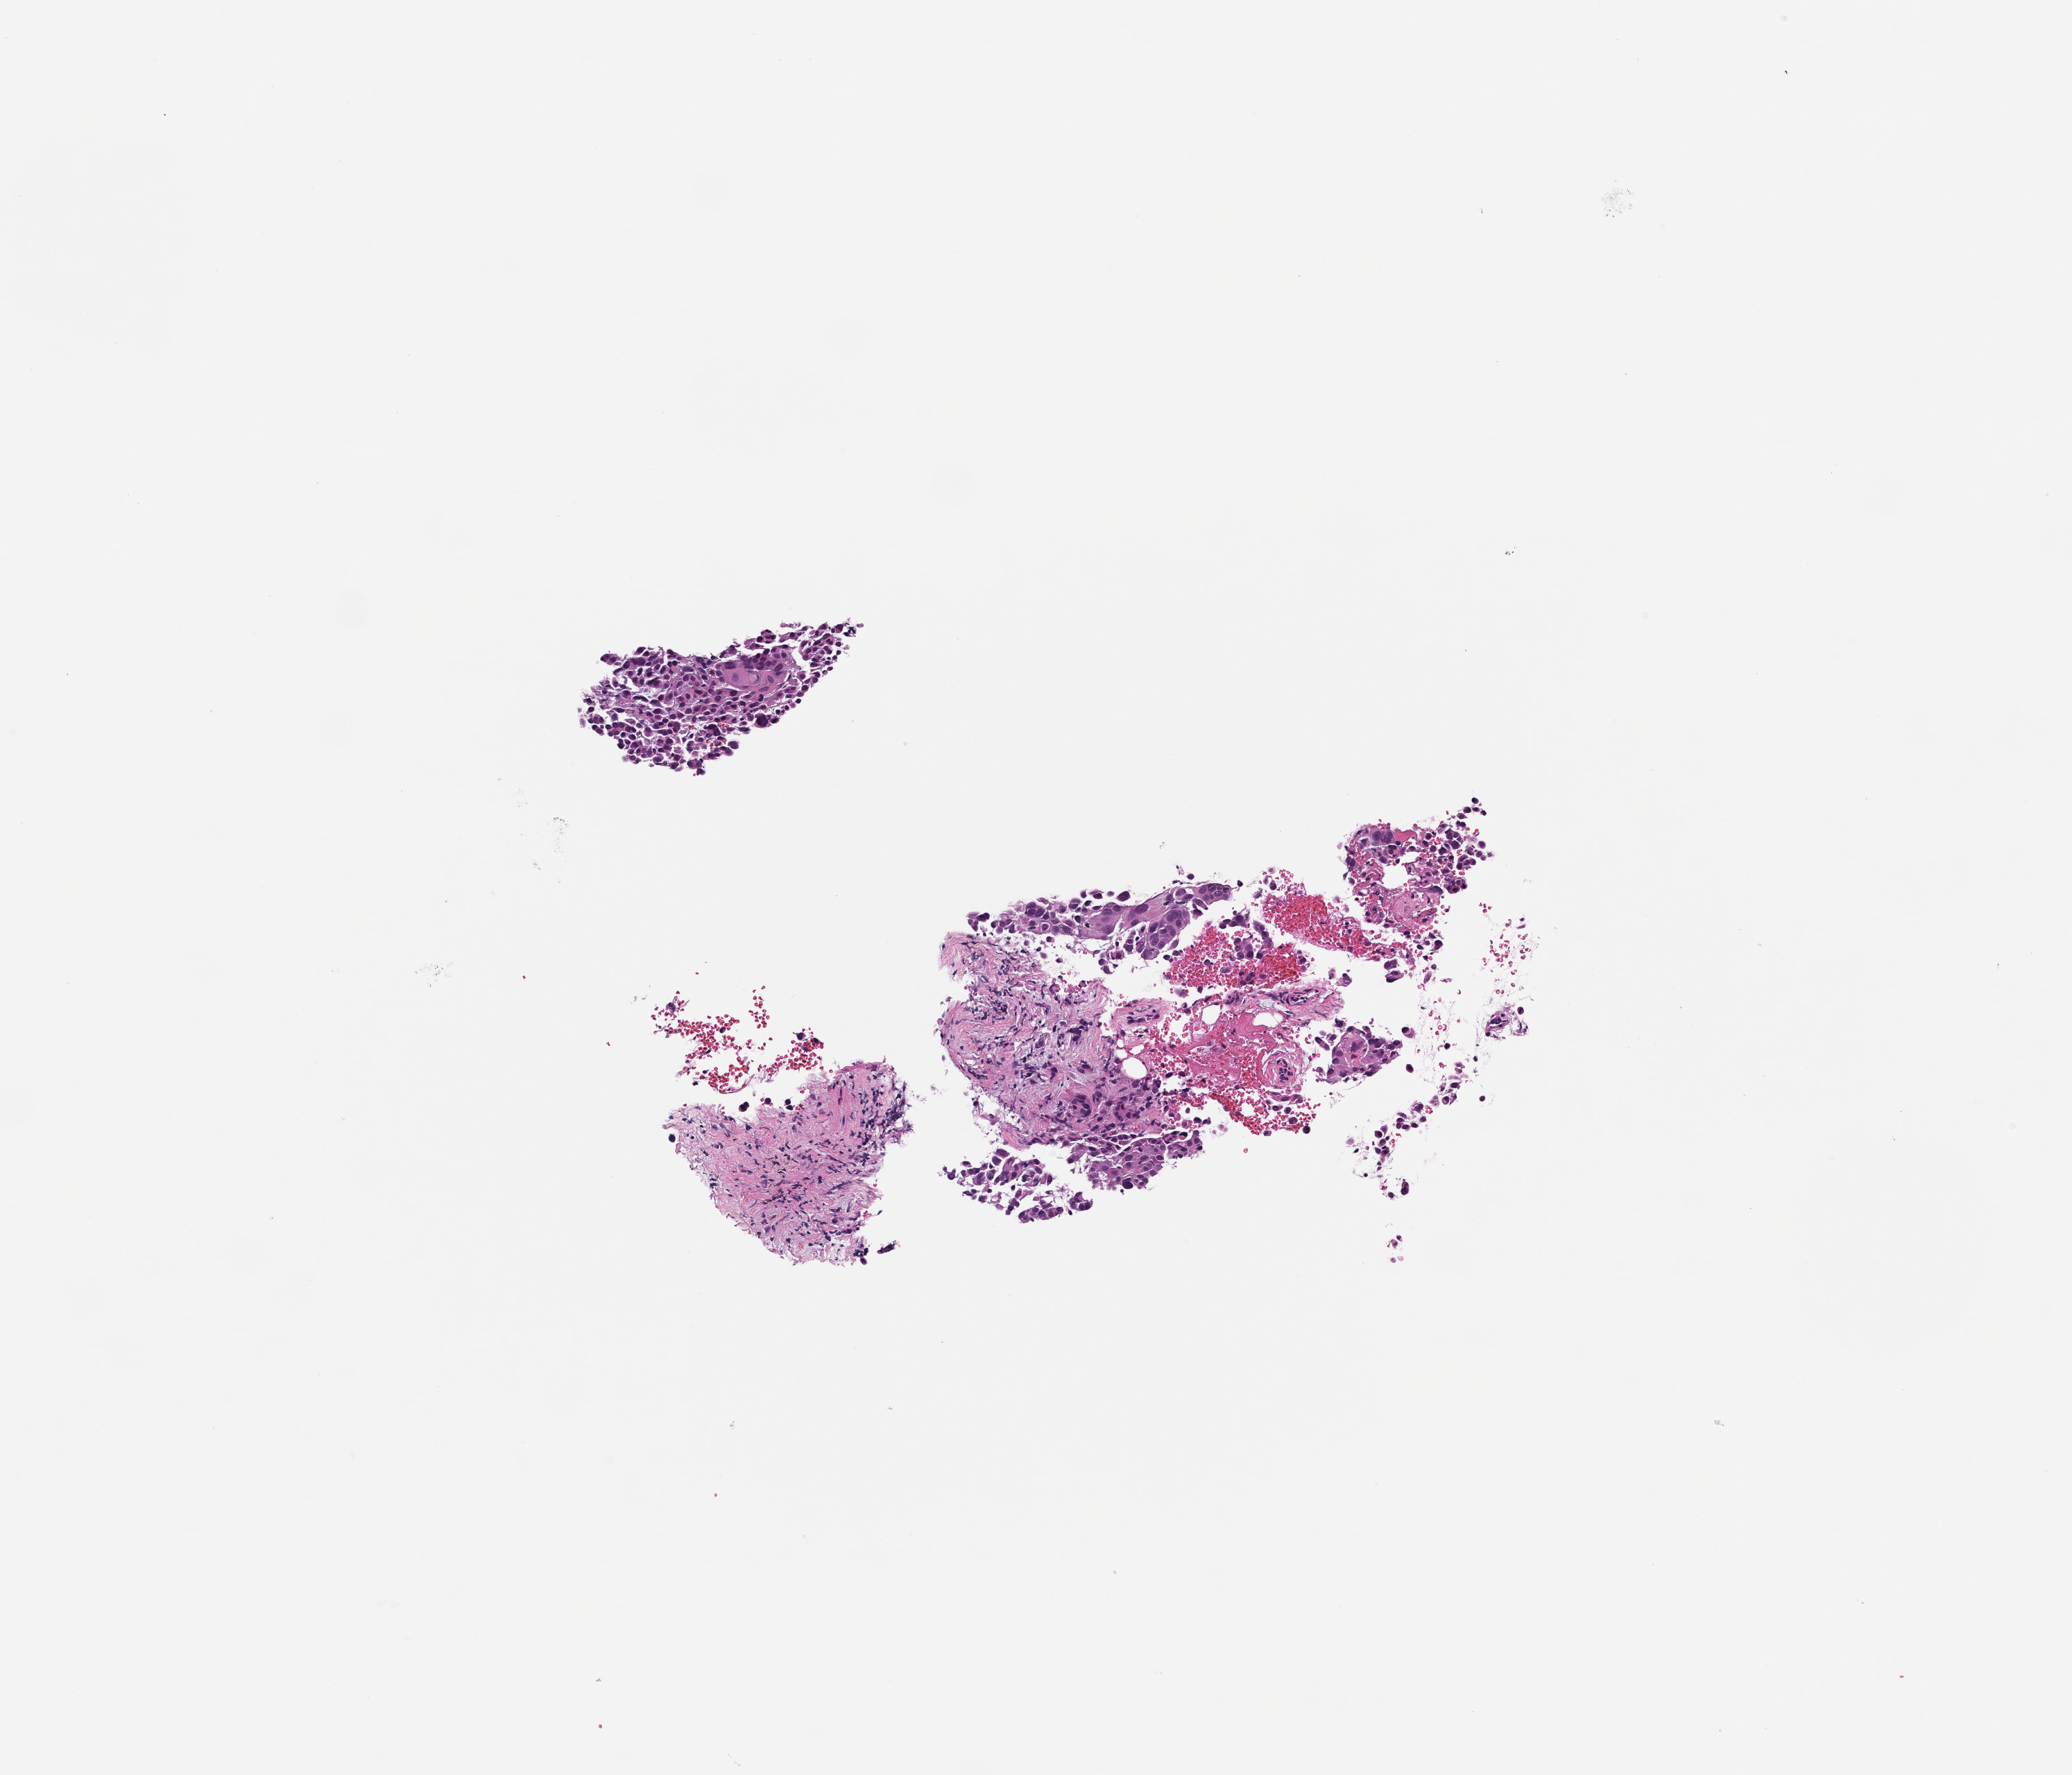
Hematoxylin and eosin (H&E) whole-slide image — shown as a low-resolution overview of the whole scanned area (about 3.0 x 2.6 mm), formalin-fixed paraffin-embedded section, site: lung, specimen time point: collected at baseline (before treatment). Patient: male.
This section: primary tumour tissue. Diagnosis: Non-Small Cell Lung Carcinoma.